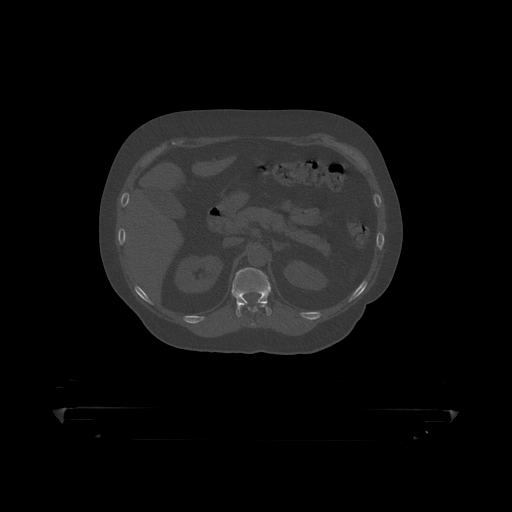
CT including the spine, one axial slice. Slice 180 of 390 in the series (ordered by position). Bone window (W 1800 / L 400 HU). 512 × 512 image matrix. Male patient, age 60 years. From the clinical record (not read from this slice): primary cancer: prostate.
Structures marked on this image (semi-automatic segmentation, software-assisted and operator-edited):
- T11 vertebra: bounding box [x1, y1, x2, y2] px = [242, 304, 267, 314]
- T12 vertebra: [232, 268, 272, 317]